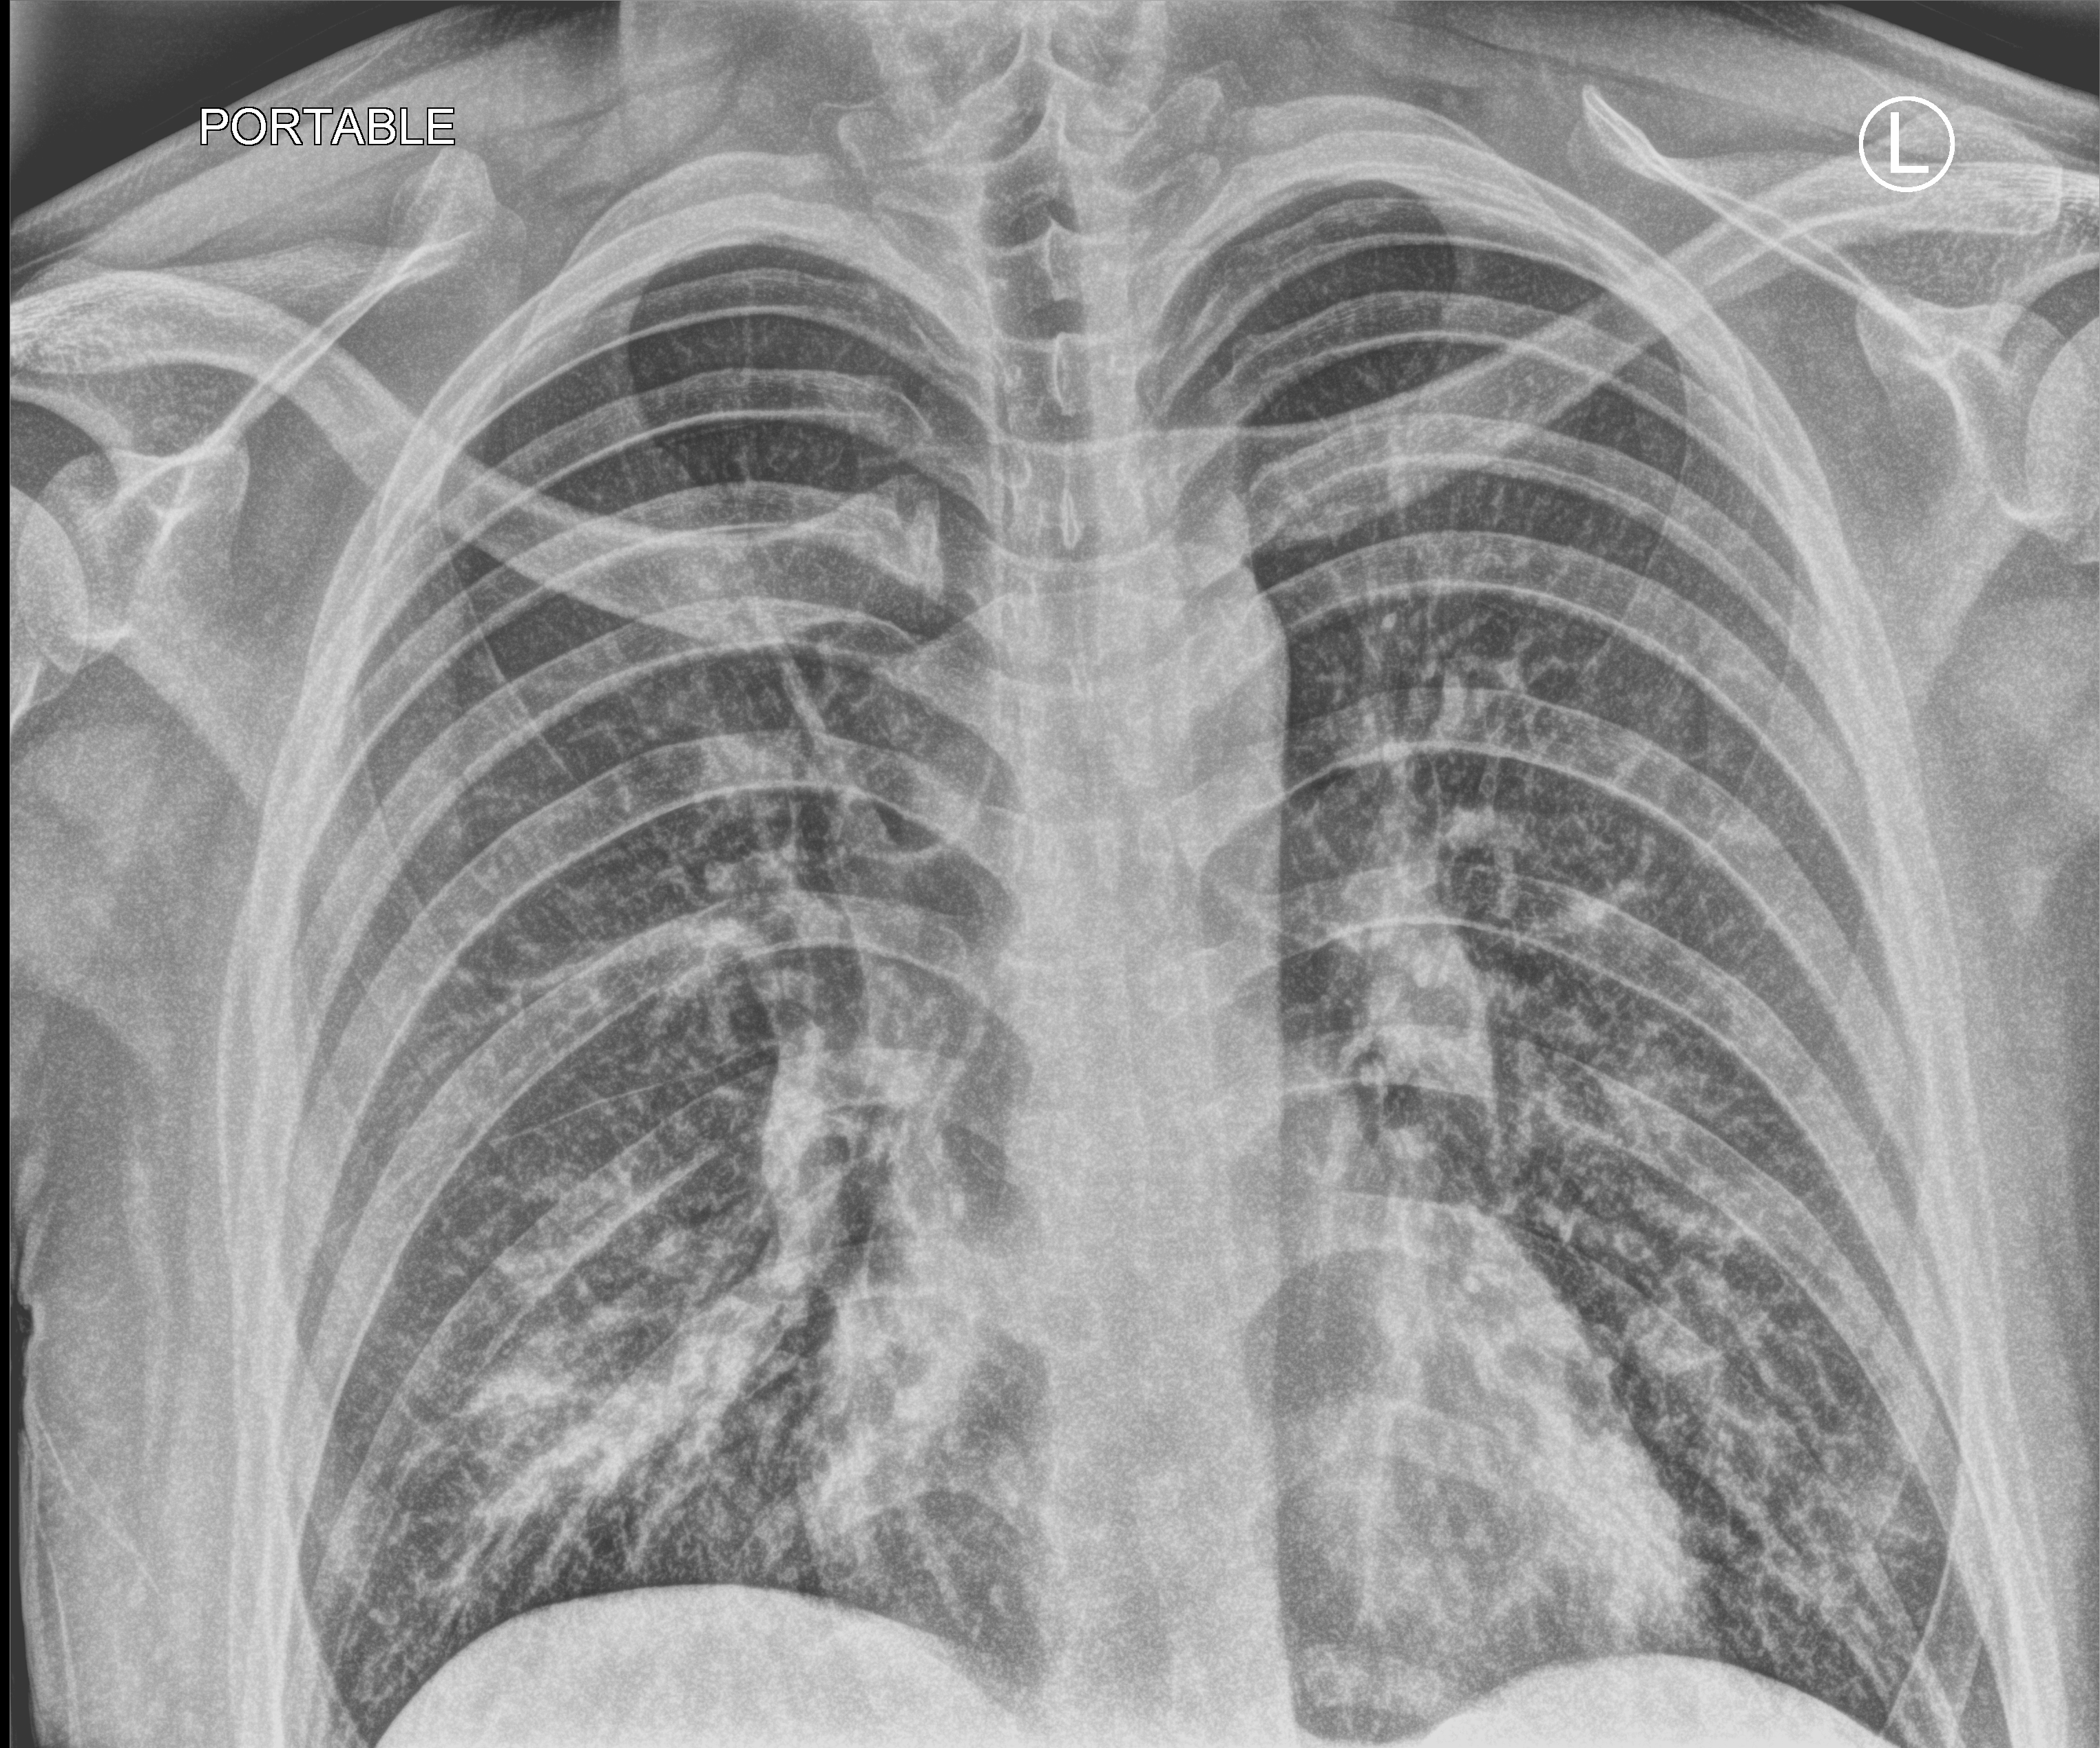
Chest X-ray (portable); anteroposterior (AP) projection. Patient hospitalised with COVID-19; male, aged 18–59 years.
Hospital-stay facts (about this admission, not read from this image; timing relative to this image not recorded): mechanically ventilated during this hospital stay: no; admitted to intensive care during this hospital stay: no.